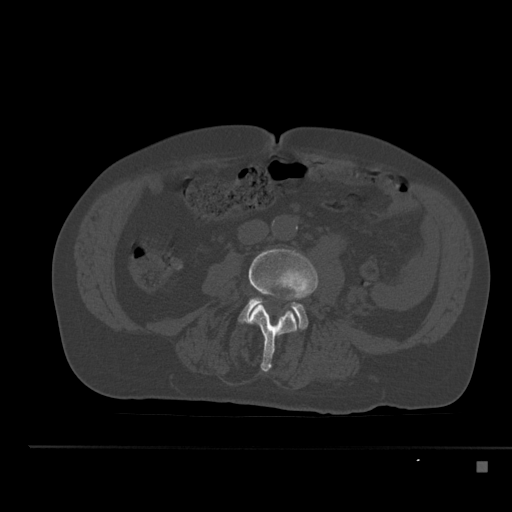
CT including the spine, one axial slice. Slice 156 of 517 in the series (ordered by position). Bone window (W 1800 / L 400 HU). 1.5 mm slice thickness. 512 × 512 image matrix, field of view 408 × 408 mm. Patient: male, 70 years. From the clinical record (not read from this slice): primary cancer: renal; vertebrae with lytic lesions (as recorded): T4, T6, T10, T12, L3, L4, L5.
Outlined on this slice (semi-automatically segmented with operator editing):
- L3 vertebra: bounding box (x1, y1, x2, y2) in pixels: (248, 249, 318, 372)
- L4 vertebra: (239, 299, 308, 329)